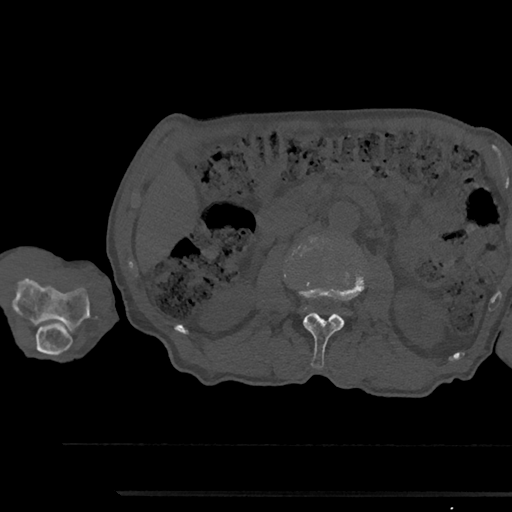
CT including the spine, one axial slice; slice 543 of 797 in the series (ordered by position); reconstruction kernel Br40s/3; 120 kVp; bone window (W 1800 / L 400 HU); 0.5 mm slice thickness; 512 × 512 image matrix. Patient: male, 79 years. From the clinical record (not read from this slice): primary cancer: prostate.
Annotated regions visible in this slice (semi-automatically segmented with operator editing):
- L2 vertebra: bounding box (x1, y1, x2, y2) in pixels: (298, 273, 365, 368)